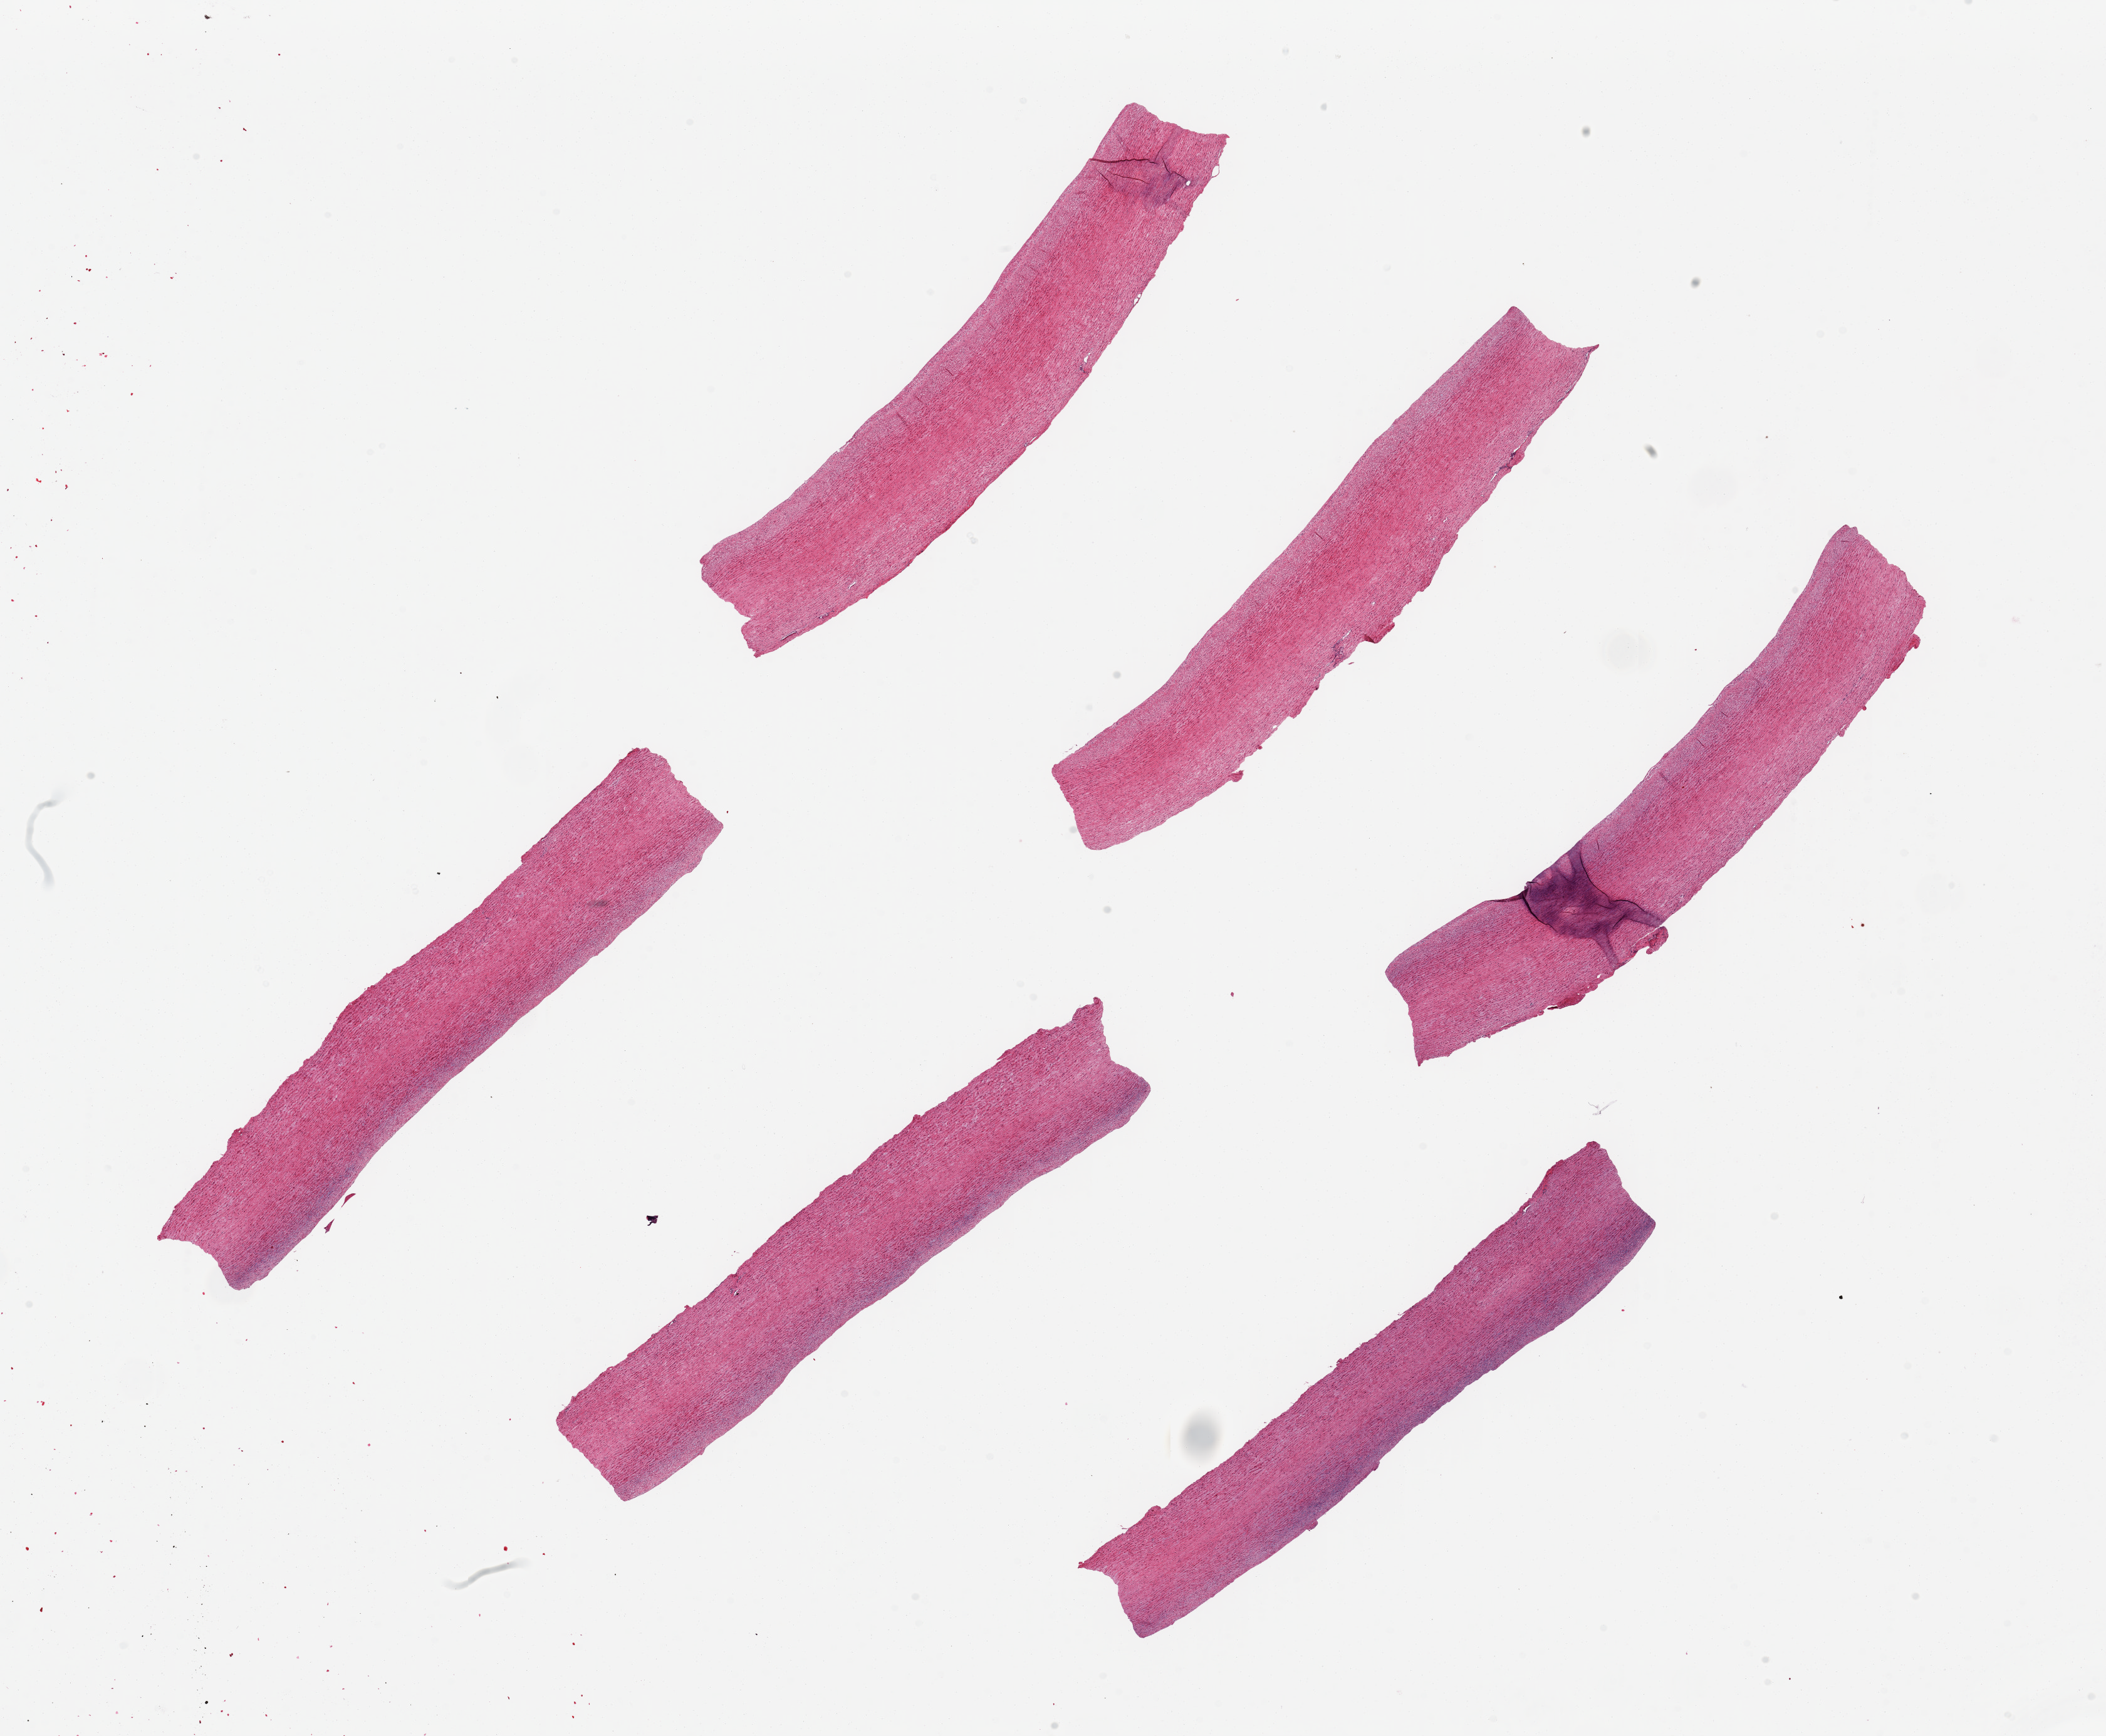
Haematoxylin and eosin whole-slide image — low-resolution overview of the scanned area, about 26.6 x 21.9 mm (acquisition: 20x scan); PAXgene-fixed, paraffin-embedded tissue; target tissue: aorta; donor tissue sample. Donor sex: male.
* reviewer comment on this tissue sample: 6 pieces up to 8.6x1.5 mm; minimal intimal thickening